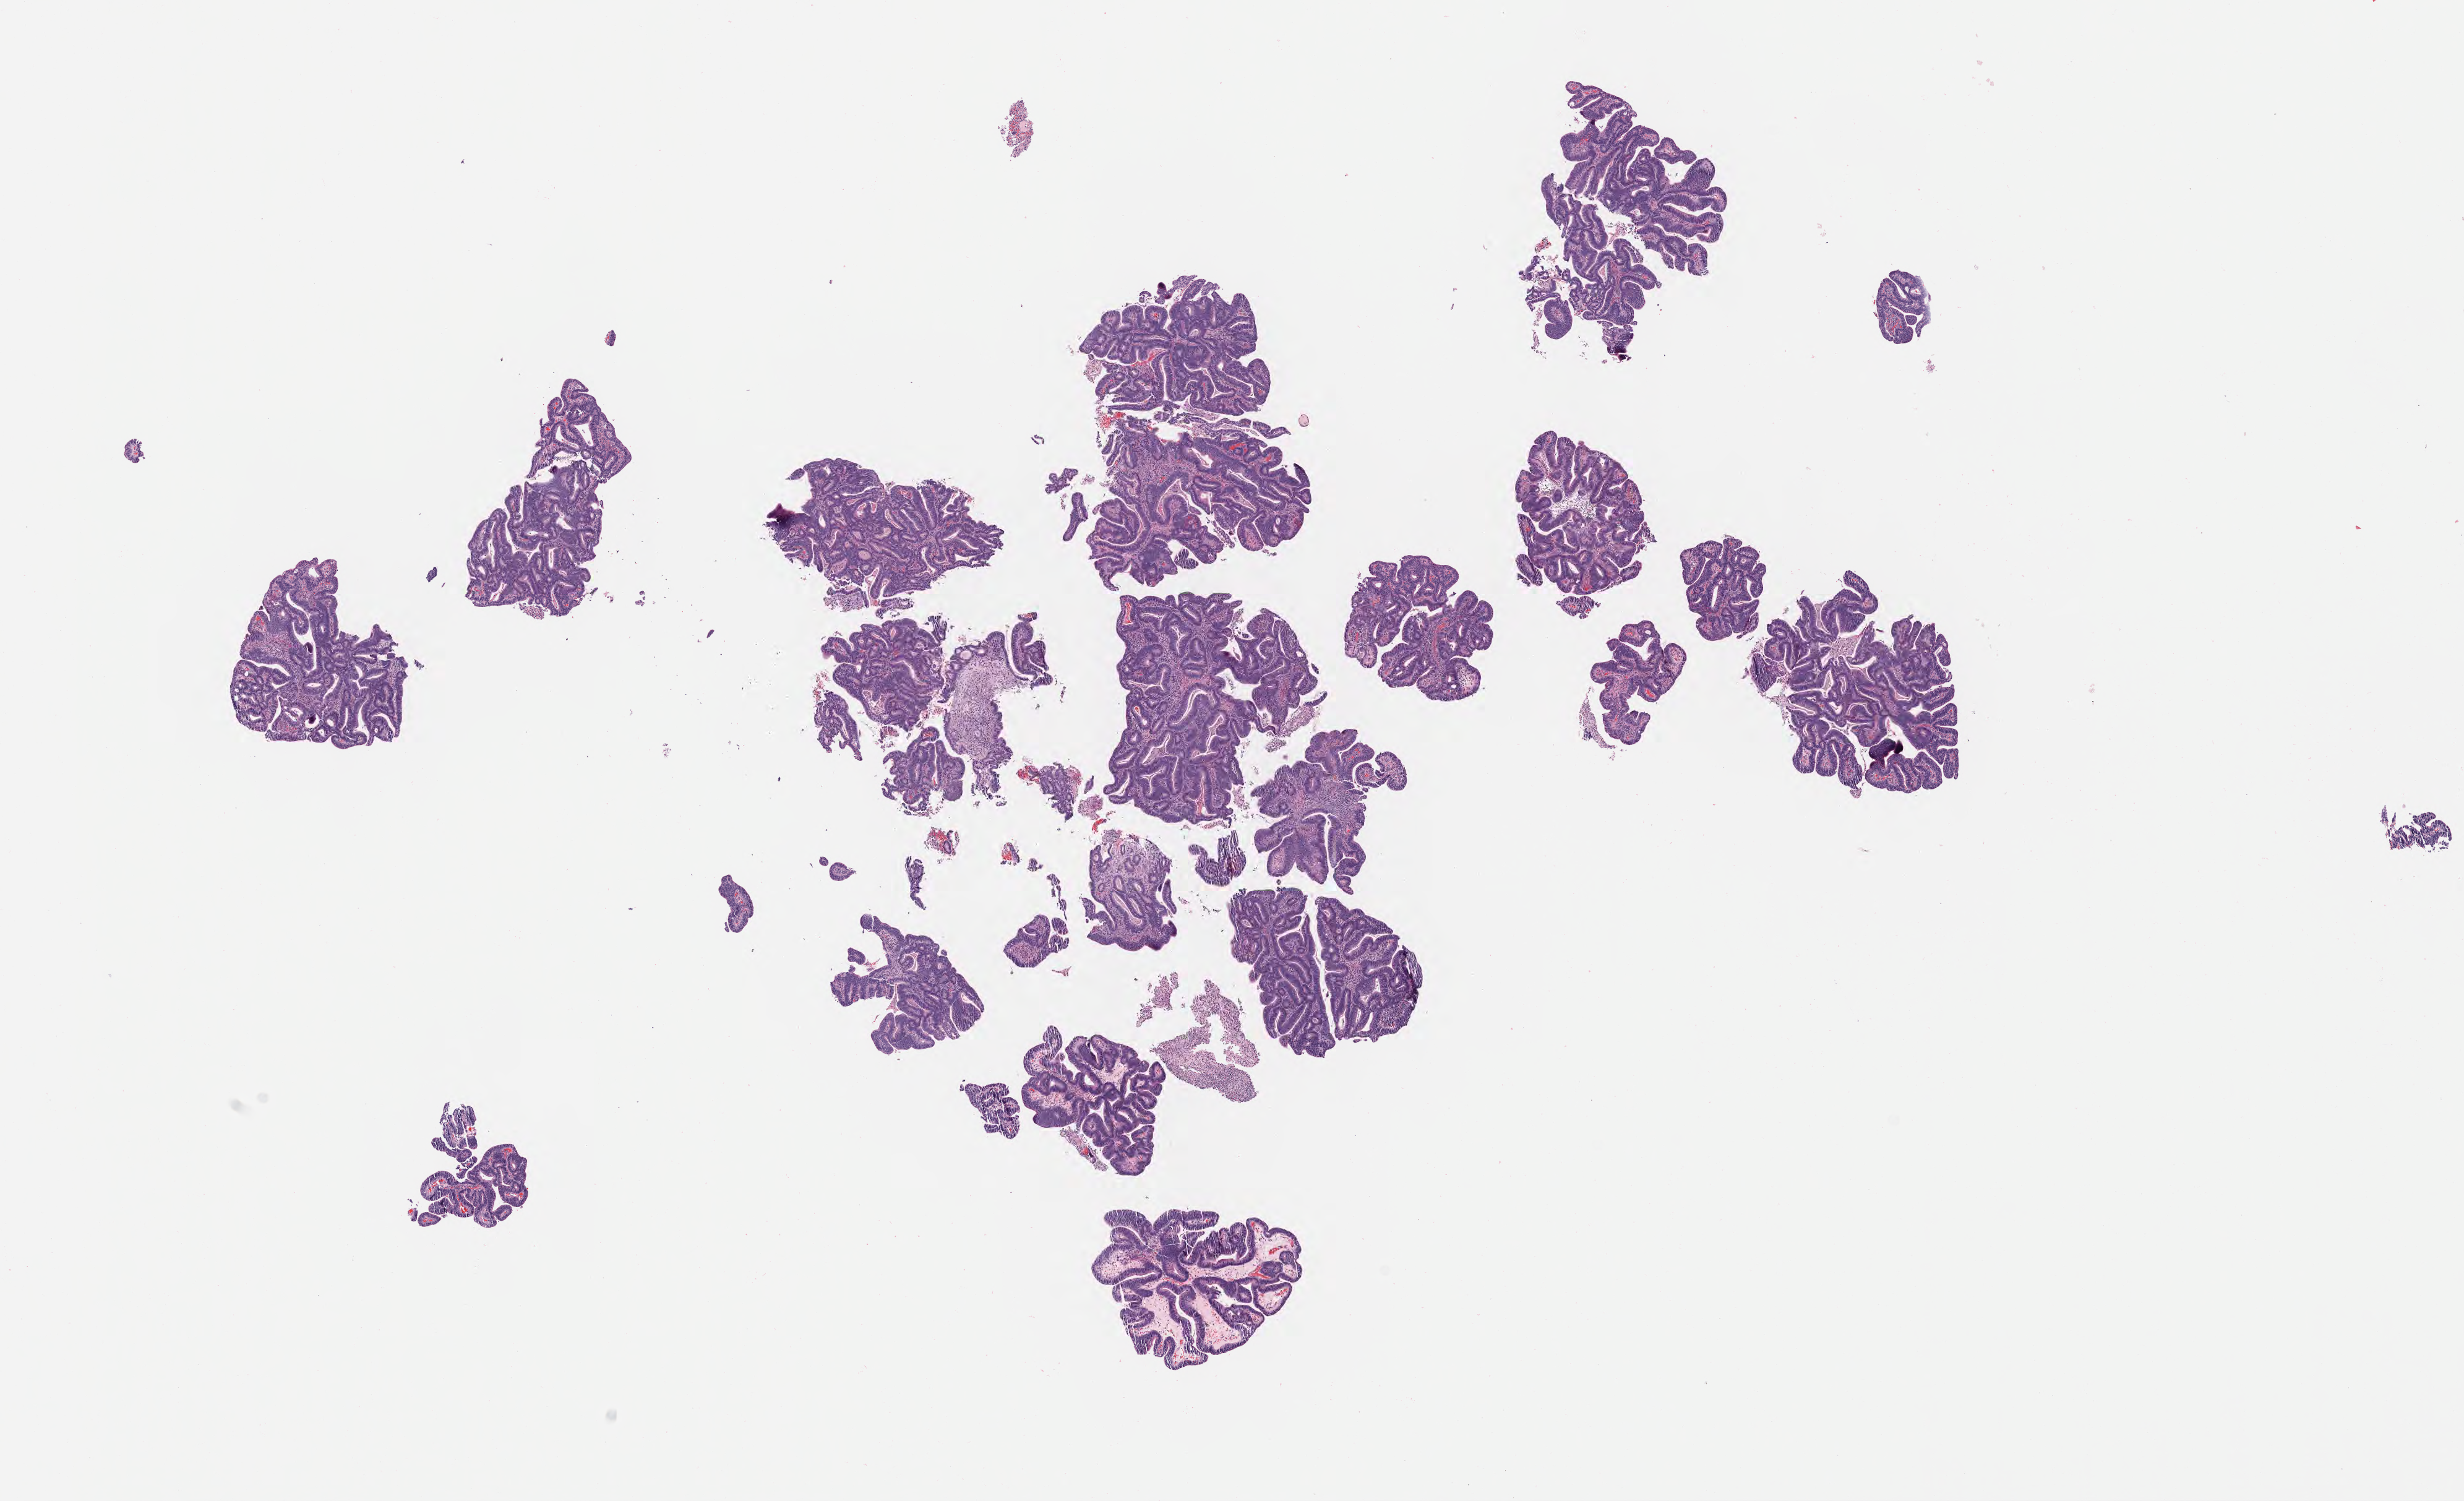
H&E whole-slide image — a low-resolution overview of the entire scanned area, about 16.1 x 9.8 mm, tumor tissue, site: cervix. Patient female; aged 33.
Diagnosis: Adenocarcinoma, NOS.